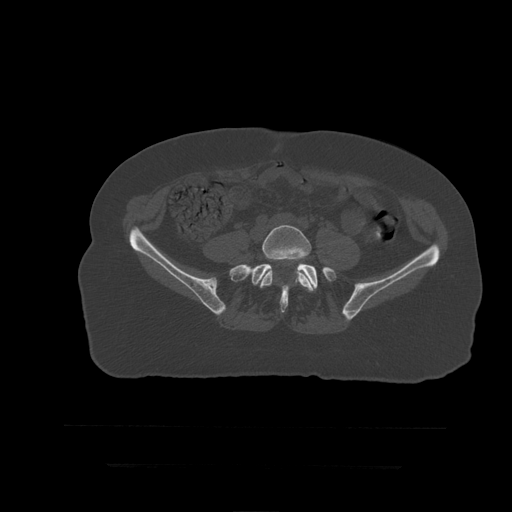
CT including the spine, one axial slice. Slice 64 of 399 in the series (ordered by position). 120 kVp. Bone window (W 1800 / L 400 HU). 512 × 512 image matrix, field of view 450 × 450 mm. Patient age 41 years. Case-level facts recorded for this patient, not image findings: primary cancer: breast.
Annotated regions visible in this slice (semi-automatic segmentation, software-assisted and operator-edited):
- L5 vertebra: bounding box <260,225,315,292> (left, top, right, bottom; pixels)